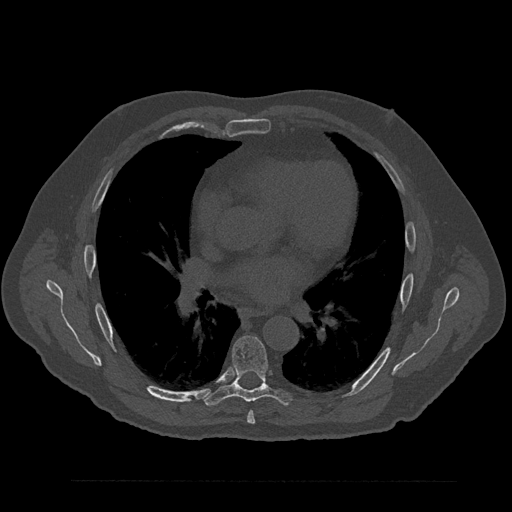
CT including the spine, one axial slice; slice 513 of 797 in the series (ordered by position); 120 kVp; bone window (W 1800 / L 400 HU); 512 × 512 image matrix, field of view 430 × 430 mm. Male patient, age 61 years. From the clinical record (not read from this slice): primary cancer: prostate.
Structures marked on this image (semi-automatic segmentation, software-assisted and operator-edited):
- T6 vertebra: bounding box <247,411,255,424> (left, top, right, bottom; pixels)
- T7 vertebra: <204,336,292,406>